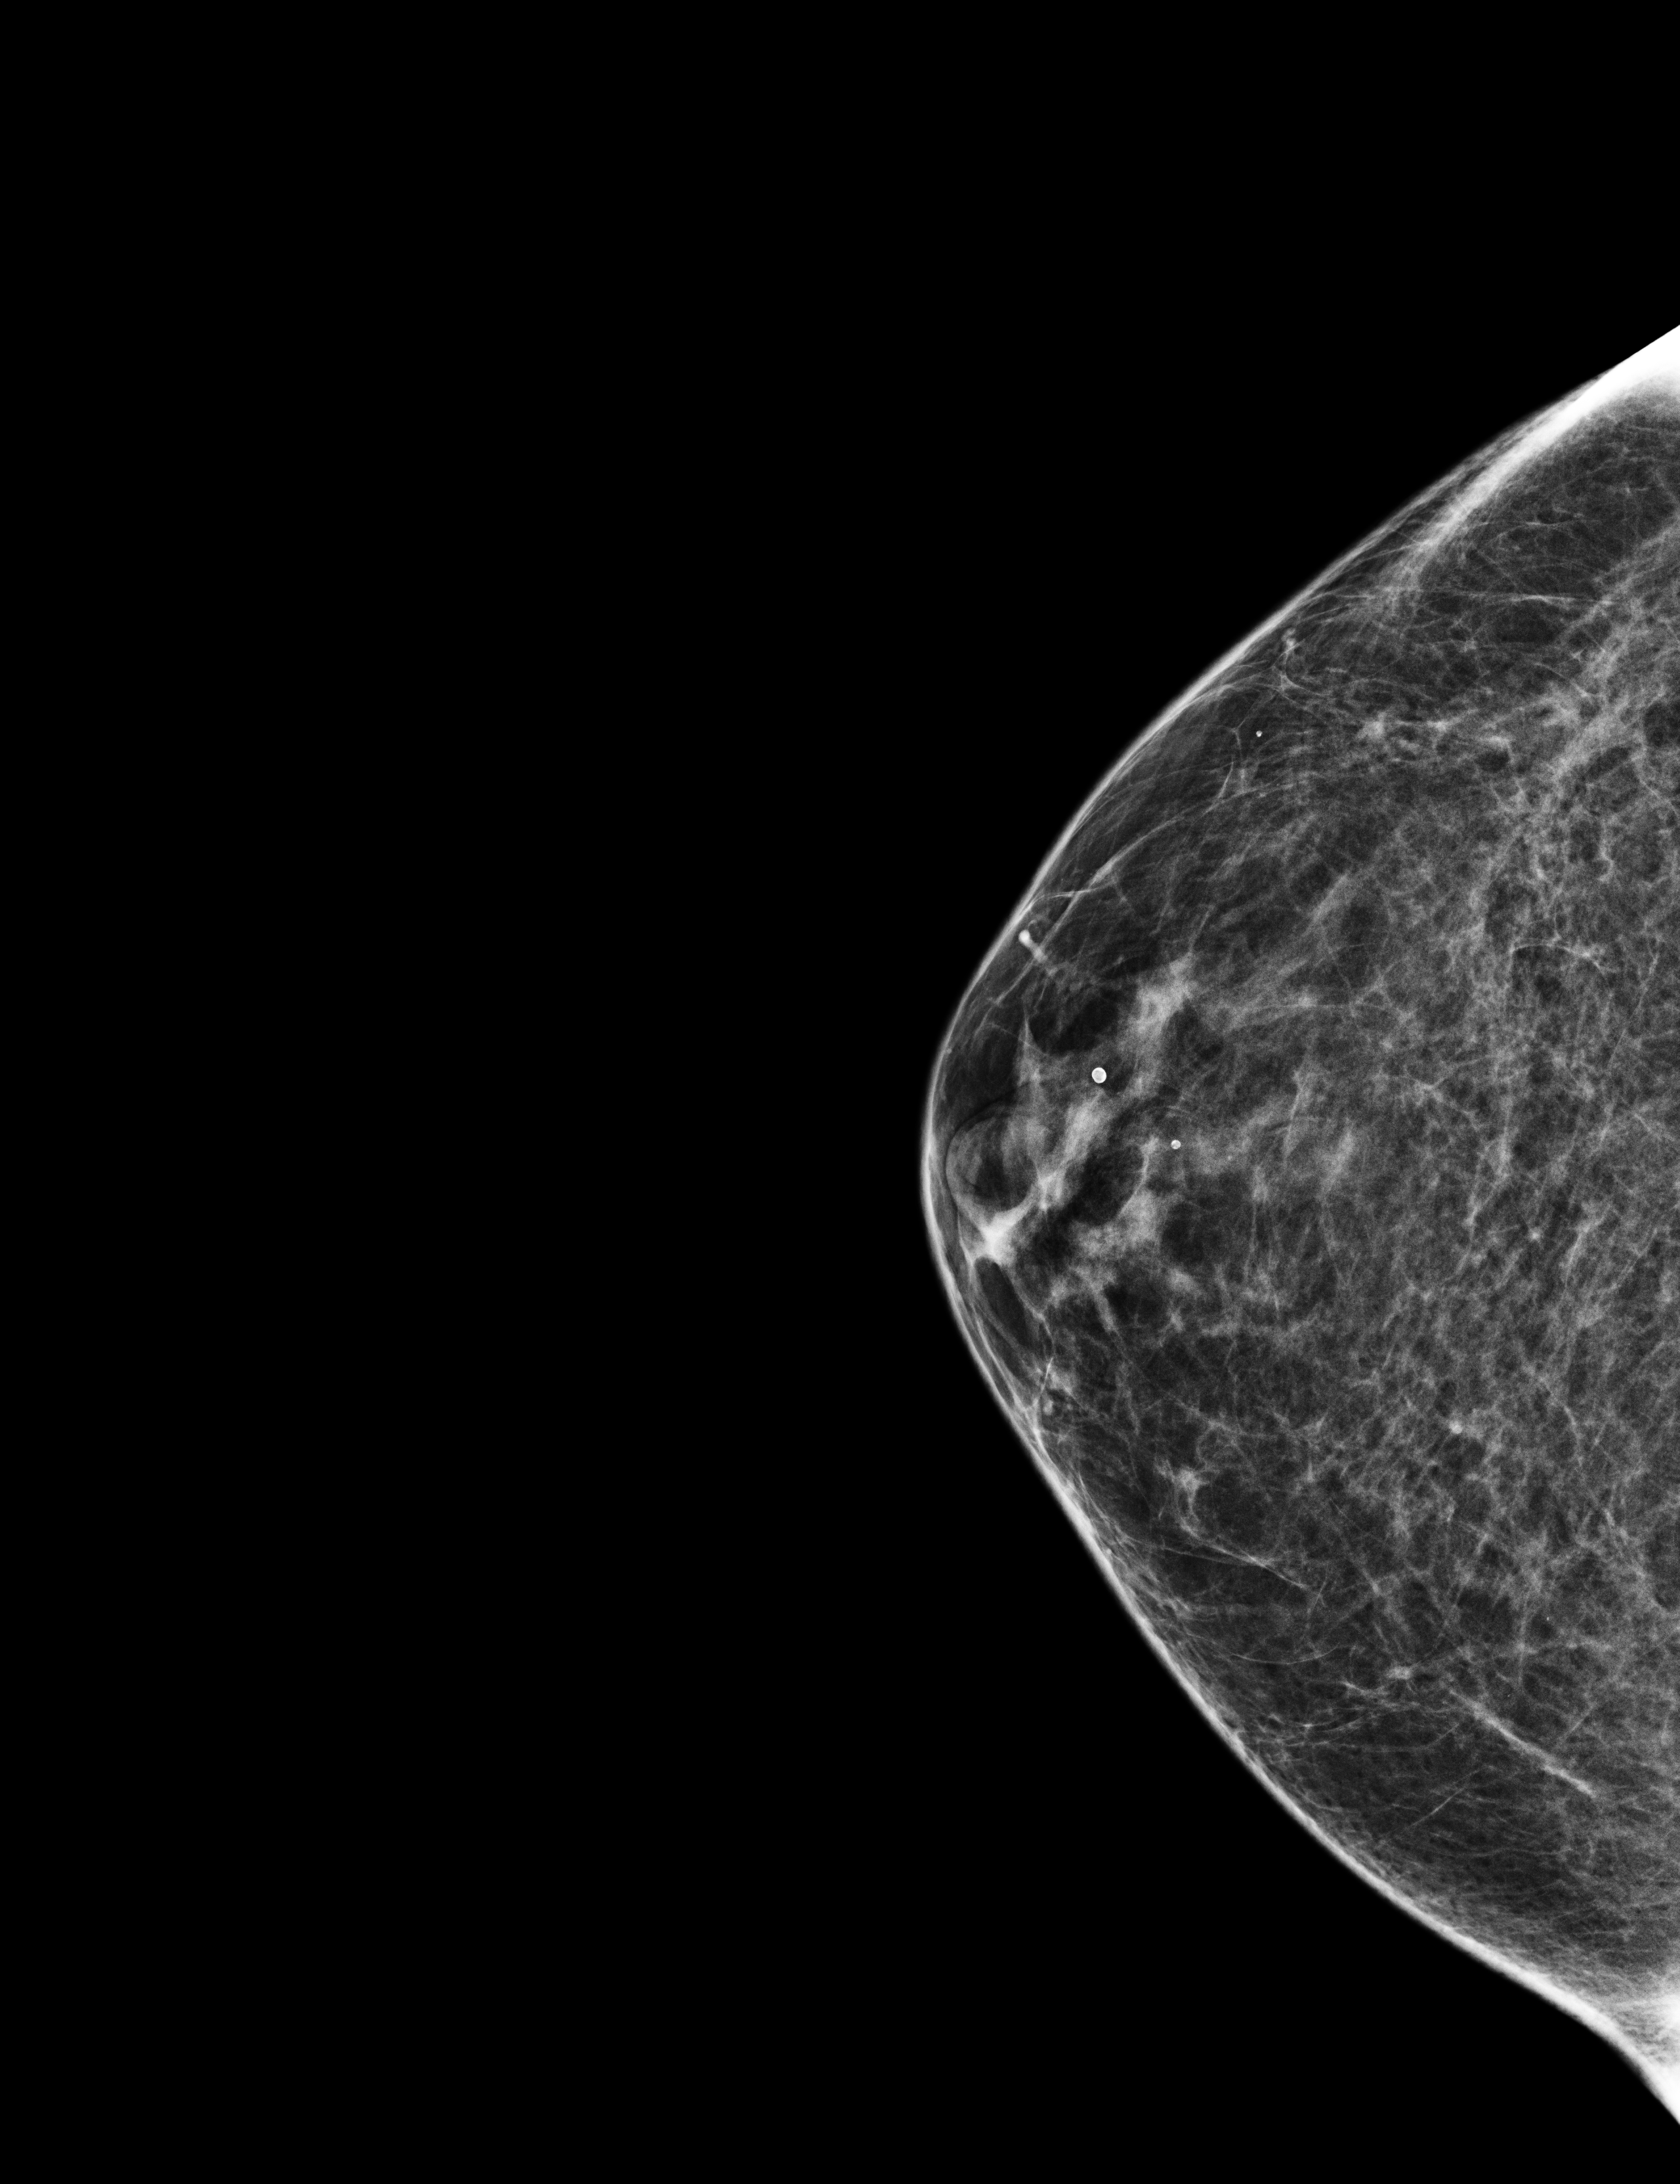
Annual screening mammography examination. Patient aged 52 years (female).
Image type: full-field digital mammogram. Breast: right. Projection: cranio-caudal projection.